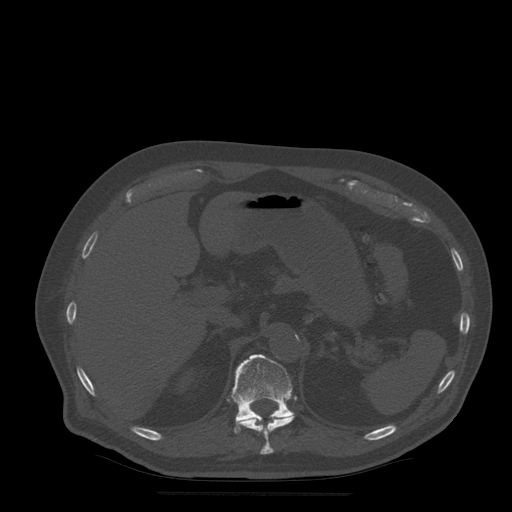
CT including the spine, one axial slice. Slice 231 of 522 in the series (ordered by position). Bone window (W 1800 / L 400 HU). 1.25 mm slice thickness. 512 × 512 image matrix. Patient age 72 years. Case-level facts recorded for this patient, not image findings: primary cancer: prostate.
Outlined on this slice (semi-automatically segmented with operator editing):
- T11 vertebra: box from (x=235, y=414) to (x=295, y=455) px
- T12 vertebra: (x=232, y=355)–(x=294, y=433)